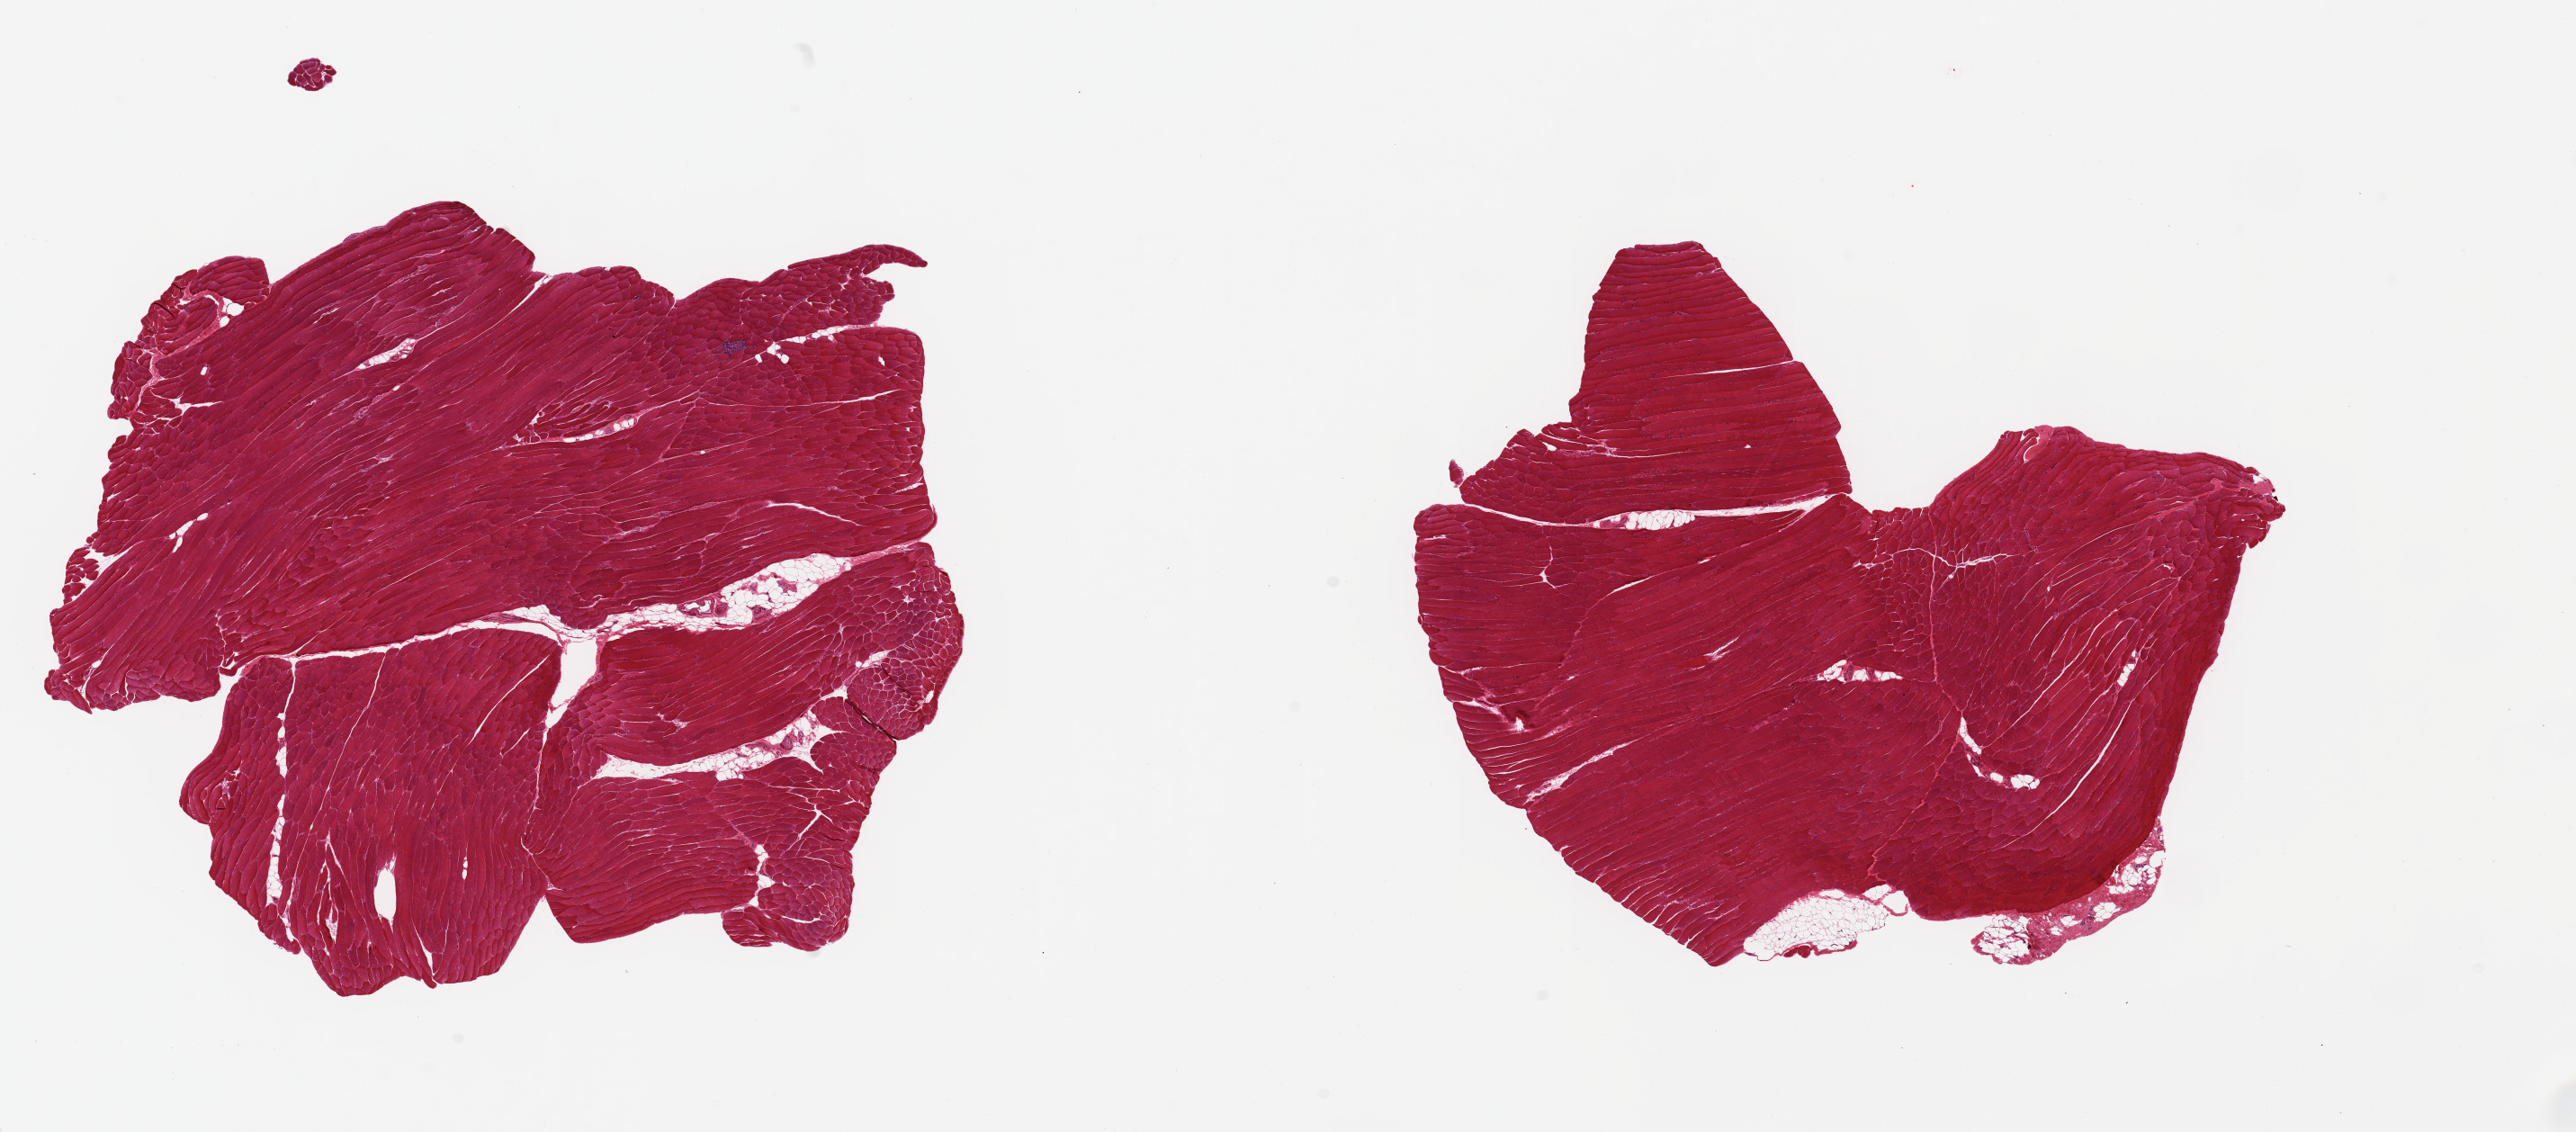
Whole-slide image, H&E stain — shown as a low-resolution overview of the whole scanned area (about 22.6 x 9.9 mm, slide scanned at 20x). PAXgene-fixed paraffin-embedded (PFPE) section. Target tissue: skeletal muscle. Donor tissue sample. Male donor.
Reviewer comment on this tissue sample: 2 pieces; <5% internal fat; well trimmed.